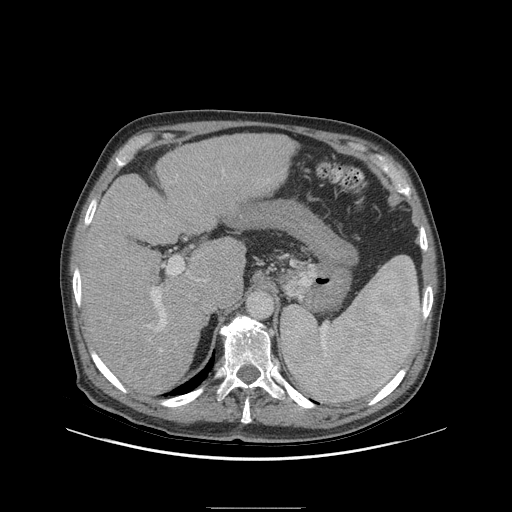
Contrast-enhanced abdominal CT (liver protocol), one axial slice; position 62 of 105 along the scan axis; reconstruction kernel STANDARD; 140 kVp; soft-tissue window (W 400 / L 40 HU); 2.5 mm slice thickness; 512 × 512 image matrix, field of view 440 × 440 mm. Case-level facts recorded for this patient, not image findings: diagnosis: hepatocellular carcinoma (patient treated with transarterial chemoembolisation; whether this scan precedes or follows treatment is not stated here); TNM stage (as recorded): Stage-I; Child-Pugh class: A; tumour nodularity: uninodular.
Structures marked on this image (semi-automatic segmentation, software-assisted and operator-edited):
- liver parenchyma outside the tumour (the mass and vessels are separate outlines, so this box may not span the whole liver): box from (x=80, y=134) to (x=294, y=394) px
- liver vessels: (x=148, y=170)–(x=224, y=351)